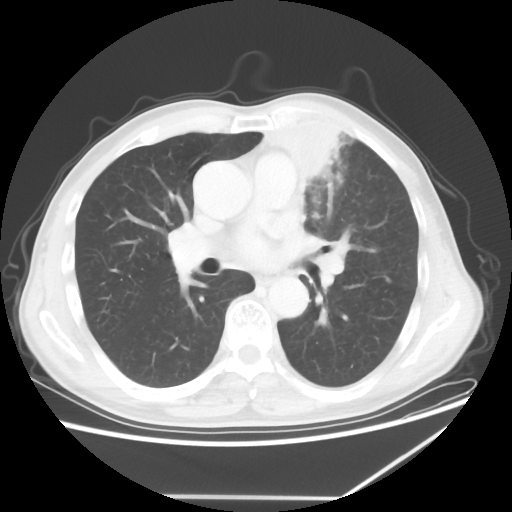
Chest CT, one axial slice. Slice 34 of 64 in the series (ordered by position). Reconstruction kernel STANDARD. Lung window (W 1500 / L -600 HU). 5 mm slice thickness. 512 × 512 image matrix, field of view 383 × 383 mm. Patient: male, 64 years. From the clinical record (not read from this slice): clinical TNM (as recorded): T1c N1 M1; histopathological grade: G2.
Structures marked on this image (bounding box drawn by a radiologist):
- lung tumour (recorded histology: squamous cell carcinoma): bounding box [x1, y1, x2, y2] px = [260, 126, 341, 208]